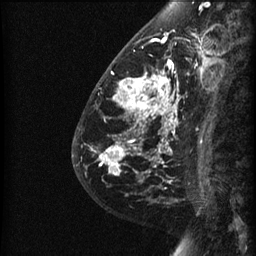
Breast MRI (dynamic contrast-enhanced), one sagittal slice; slice 18 of 60 in the series (ordered by position); dynamic contrast-enhanced series, image 2 of 3 at this slice position (ordered by acquisition); 1.5 T; TE 4.2 ms, TR 22.7 ms; 1.5 mm slice thickness; 256 × 256 image matrix, field of view 180 × 180 mm. Patient: female, 48 years. Case-level facts recorded for this patient, not image findings: setting: breast cancer imaged before/during neoadjuvant chemotherapy; receptor status: triple-negative.
Structures marked on this image (semi-automatic segmentation, software-assisted and operator-edited):
- analysis volume of interest (the breast-tissue region the enhancement analysis was run in; not a lesion): box from (x=89, y=27) to (x=191, y=180) px
- tumour enhancement mask (voxels above the 90 % enhancement threshold inside the analysis volume of interest): (x=98, y=32)–(x=189, y=180)